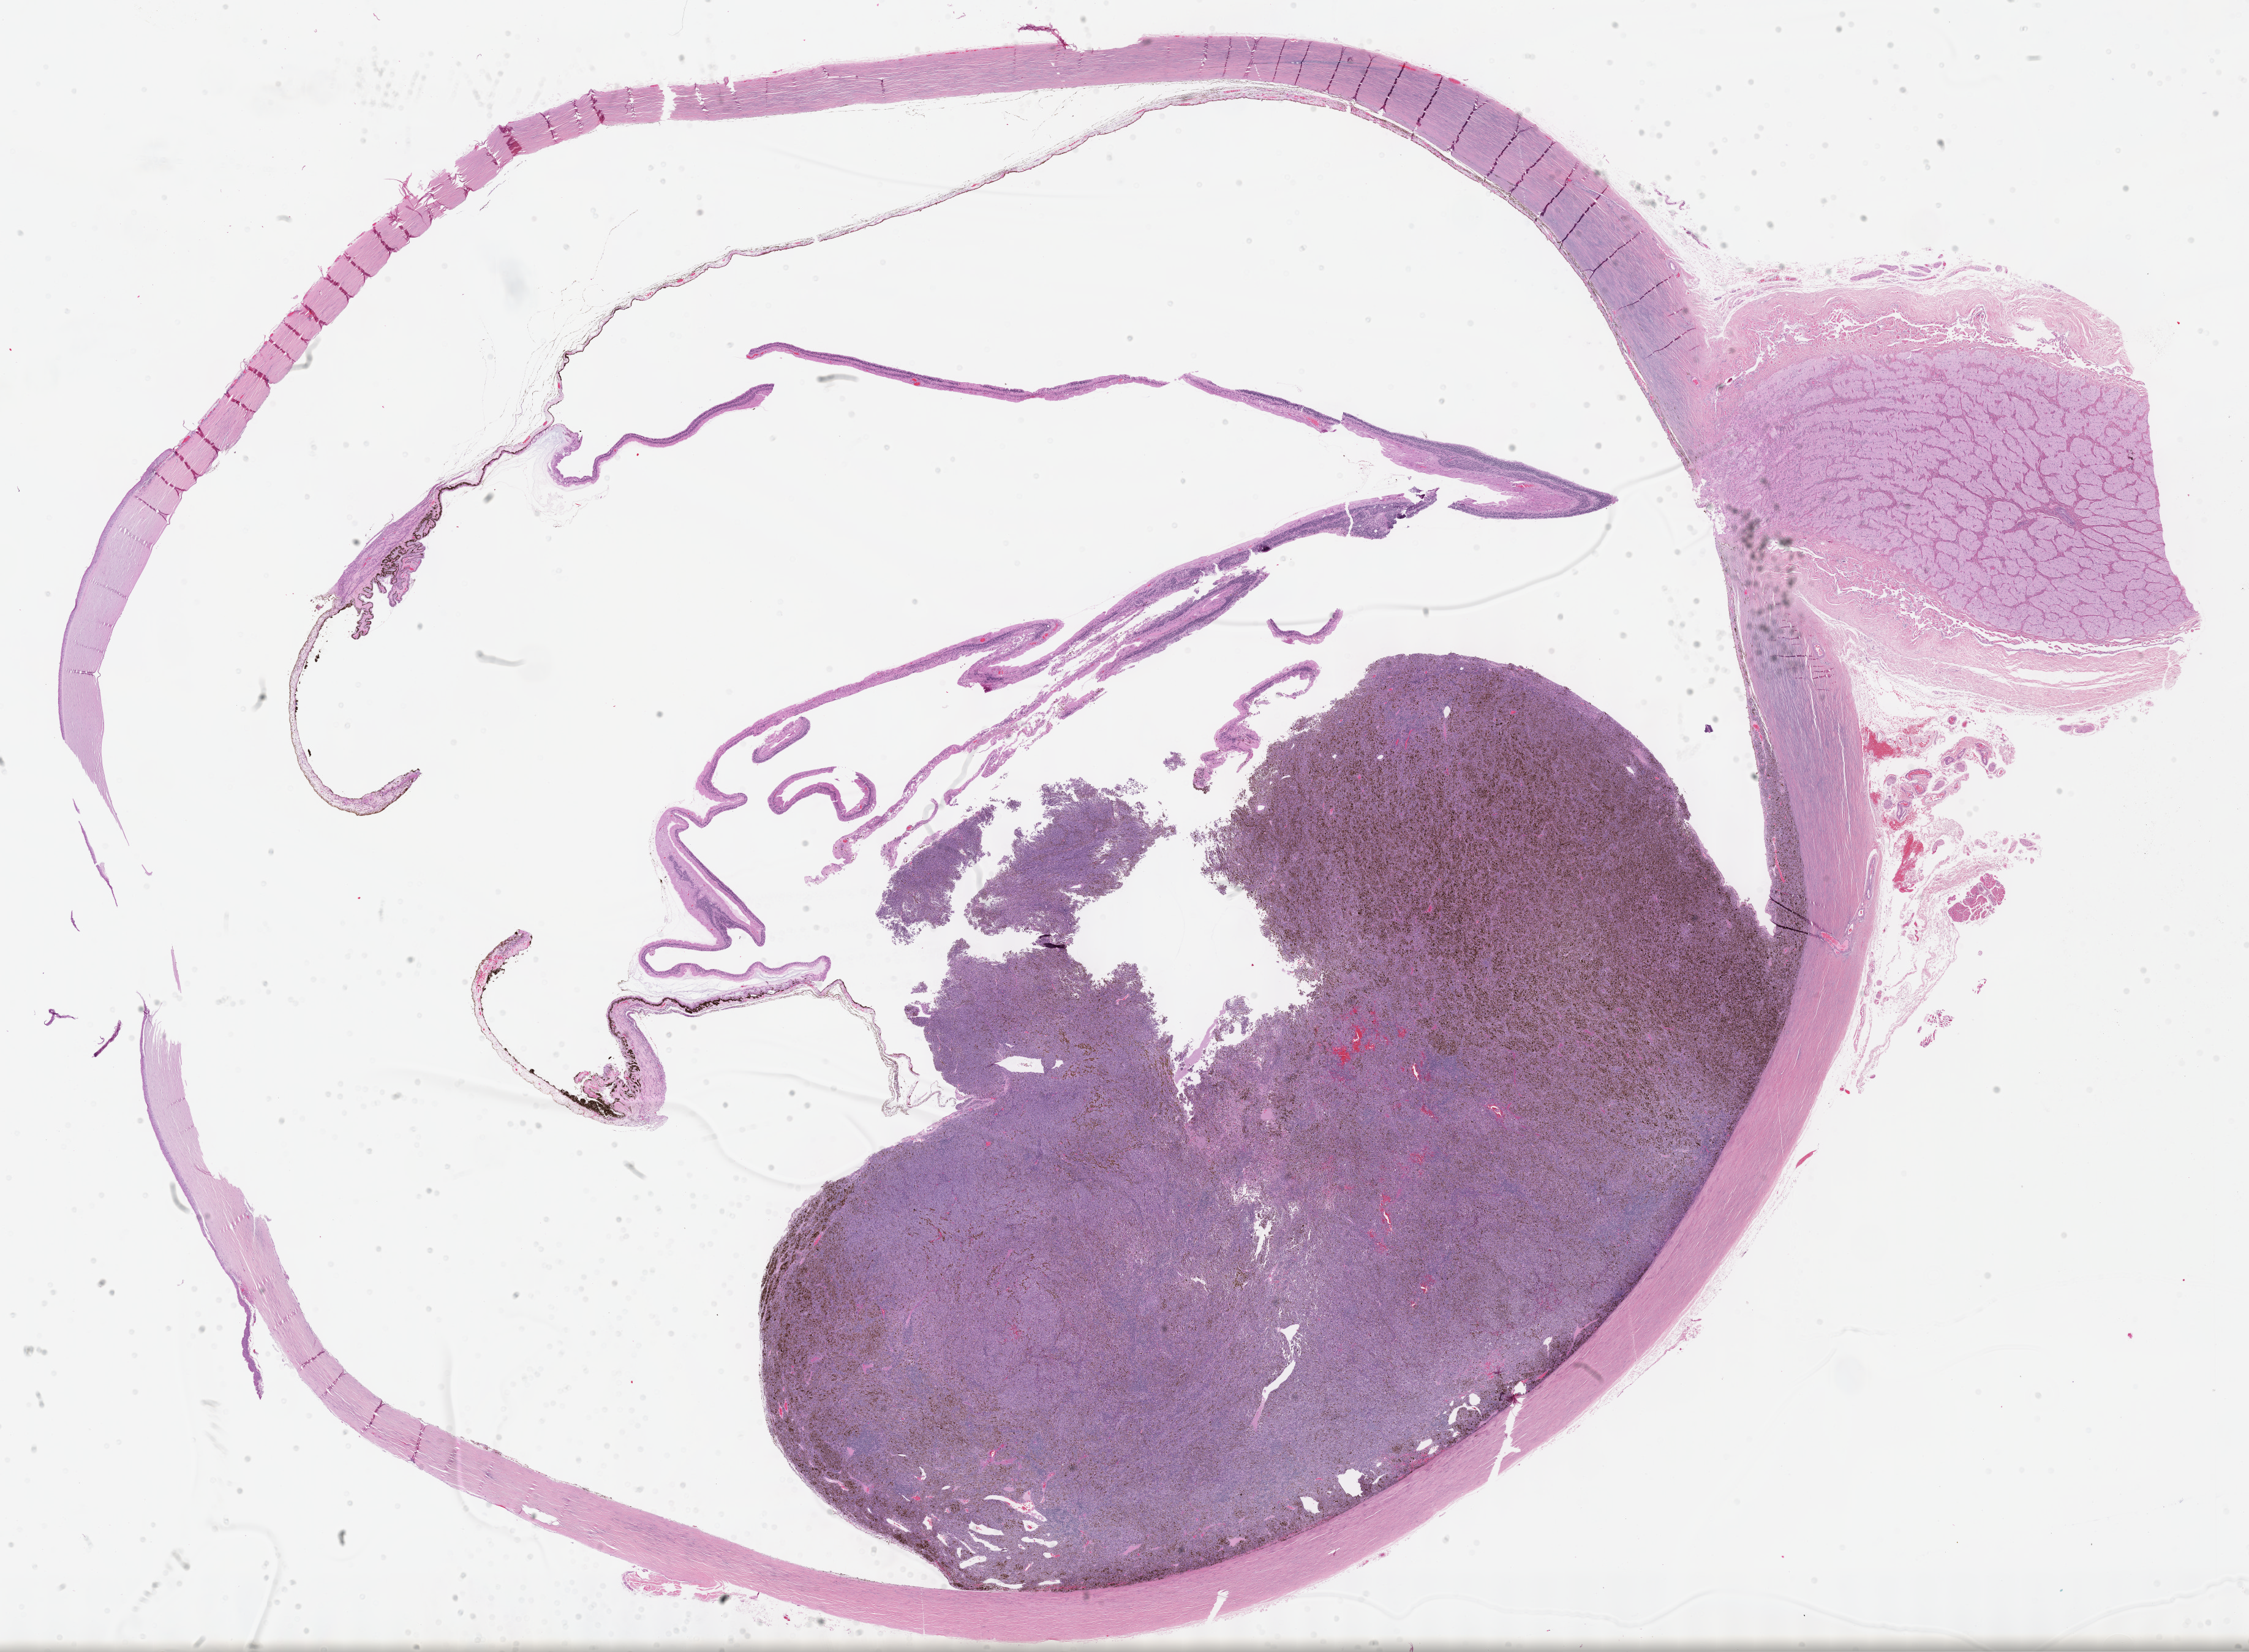
Whole-slide histology image, Hematoxylin and eosin (H&E) stained, whole scanned area (about 29.7 x 21.8 mm, acquisition: 40x scan) shown as a low-resolution overview, FFPE section, sample: primary tumour, uvea. Male patient; age at initial diagnosis 76 years.
AJCC pathologic stage: IIB. Histologic diagnosis: Mixed epithelioid and spindle cell melanoma (choroid). Laterality: right.